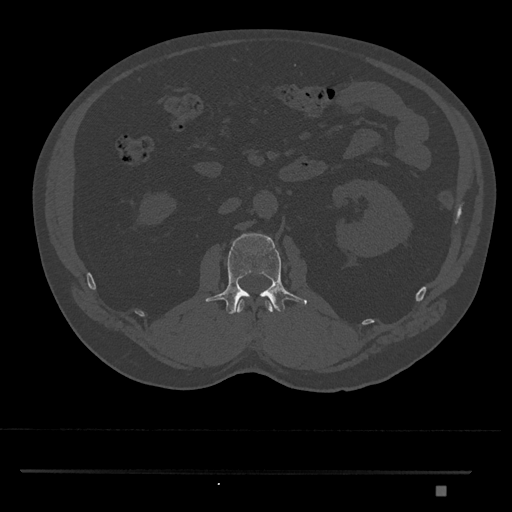
CT including the spine, one axial slice; position 765 of 1134 along the scan axis; reconstruction kernel Br40s/3; bone window (W 1800 / L 400 HU); 0.5 mm slice thickness; 512 × 512 image matrix, field of view 429 × 429 mm. Patient: male, 65 years. From the clinical record (not read from this slice): primary cancer: prostate.
Structures marked on this image (semi-automatically segmented with operator editing):
- L1 vertebra: bounding box (x1, y1, x2, y2) in pixels: (234, 299, 274, 314)
- L2 vertebra: (205, 233, 307, 314)